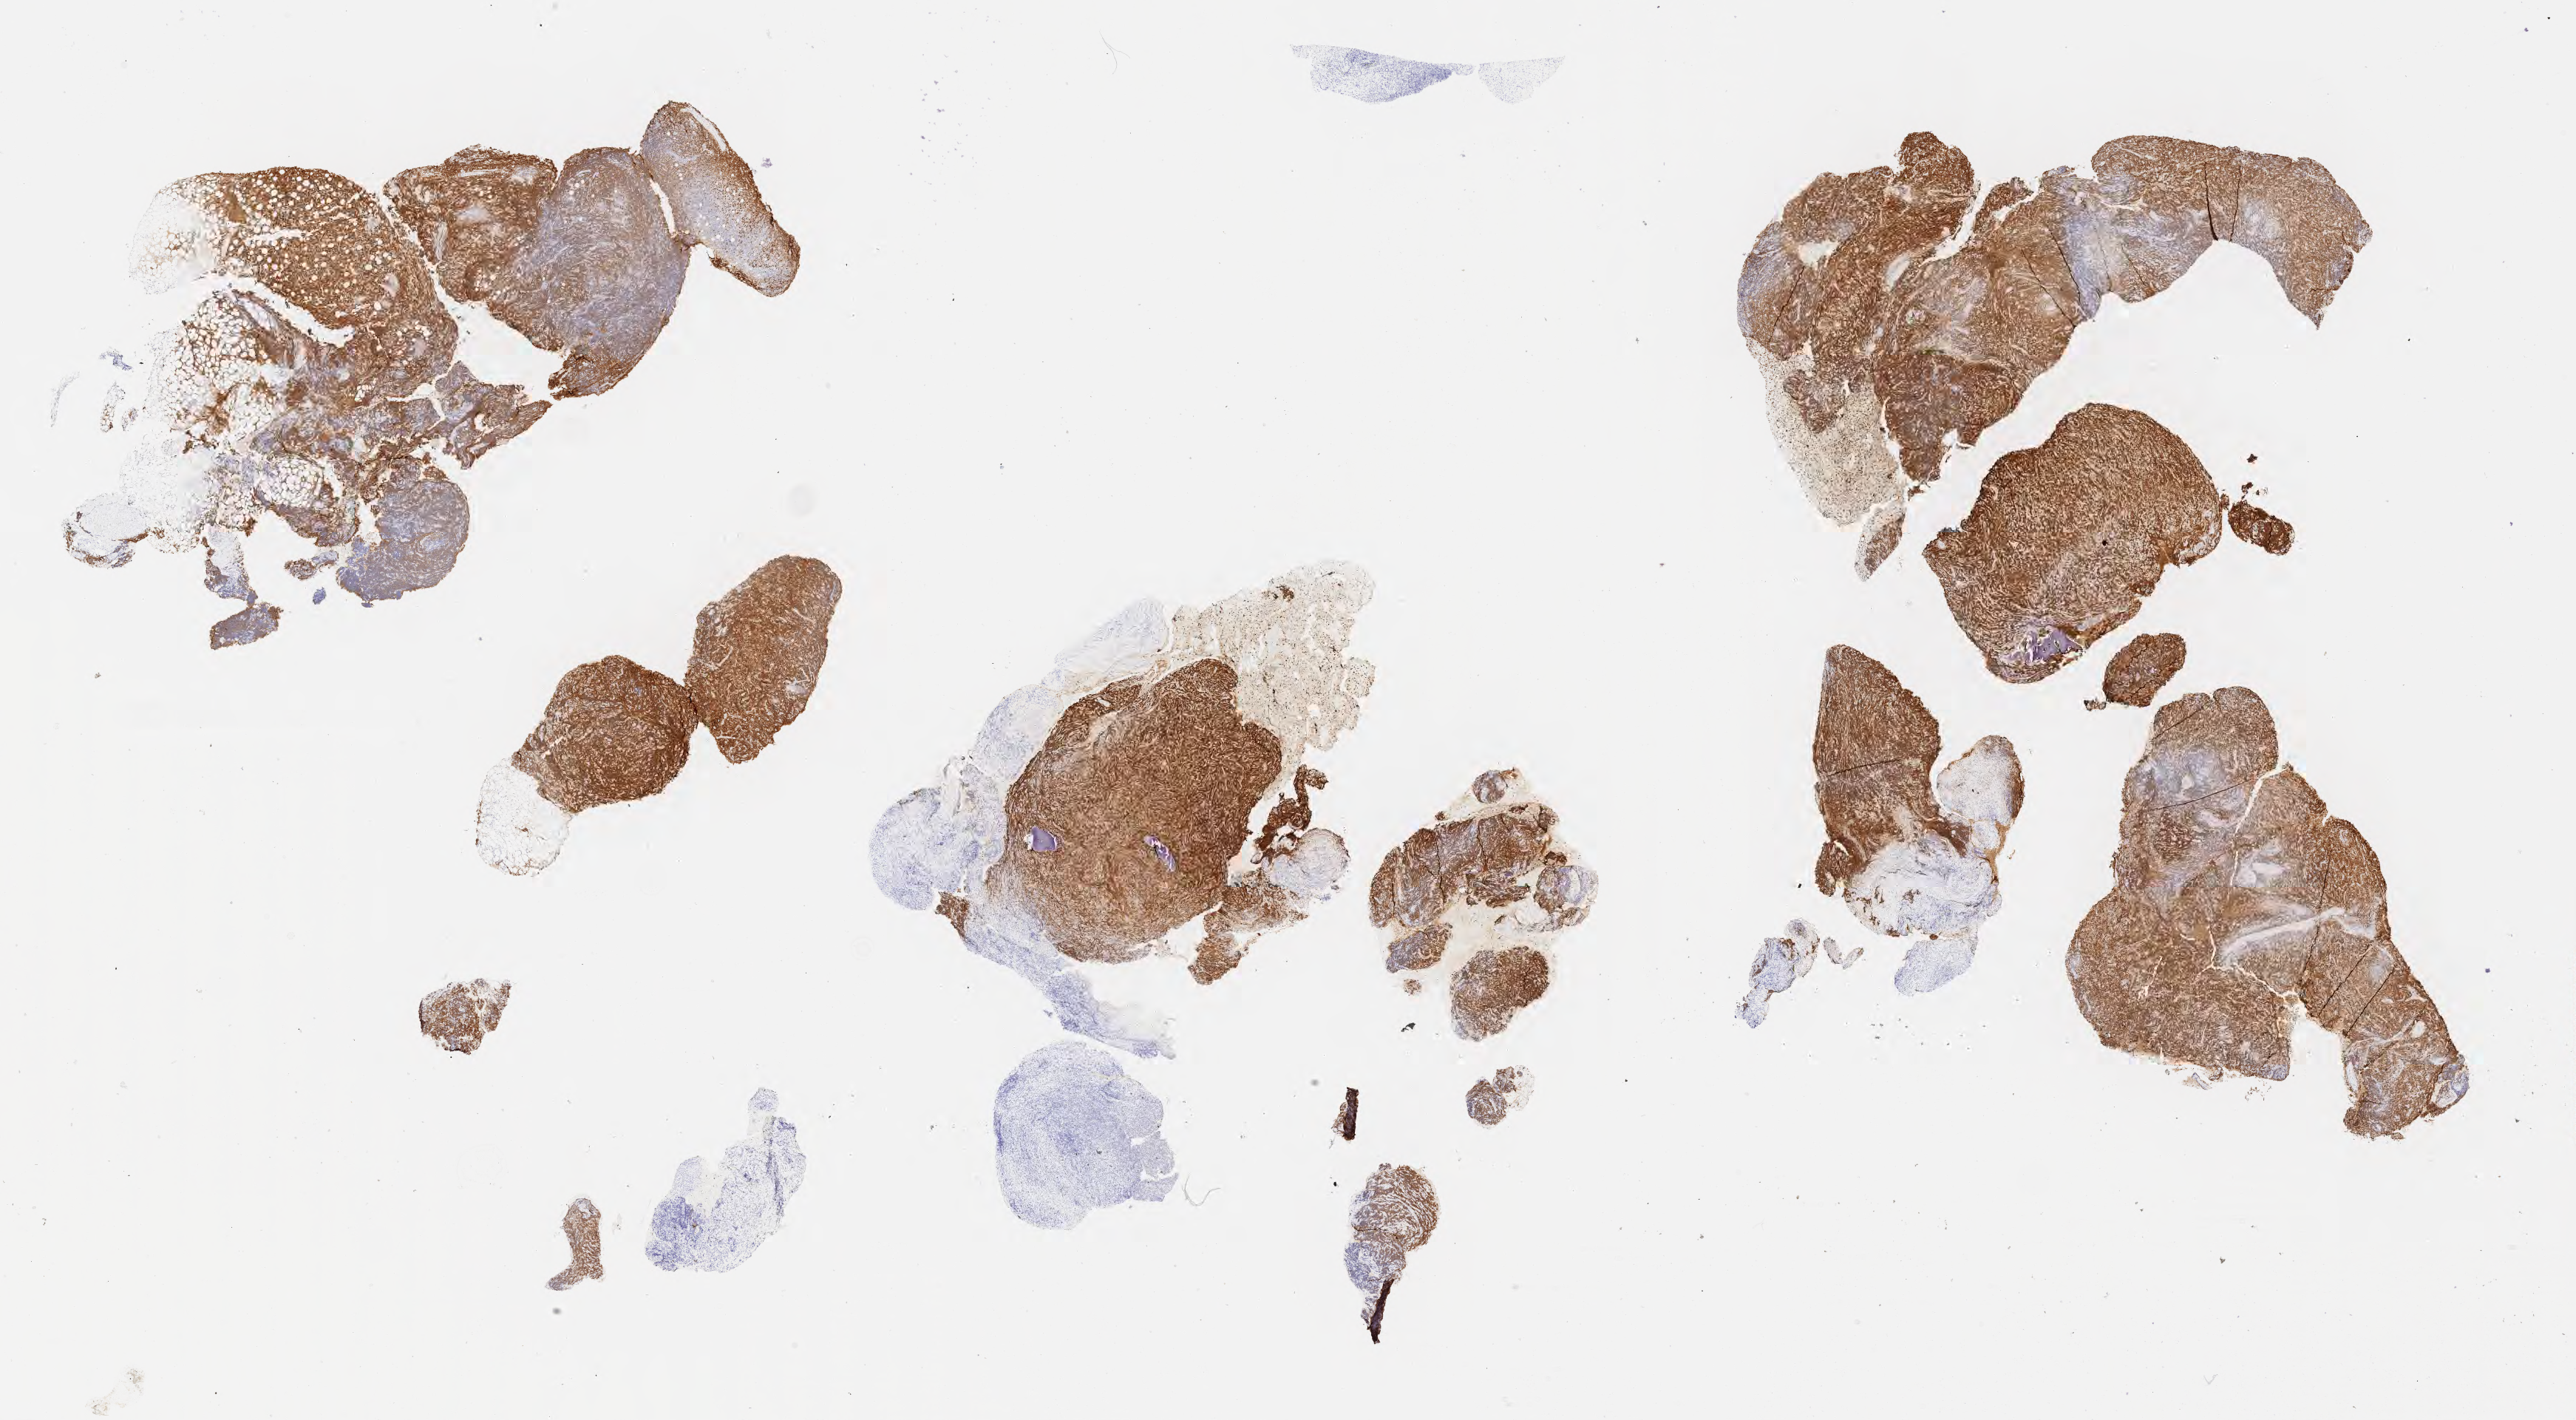
Whole-slide image, immunohistochemical stain for BCL6 — a low-resolution overview of the entire scanned area, about 28.2 x 15.5 mm; tumor tissue. Patient male; aged 45.
Diagnosis: Diffuse large B-cell lymphoma, NOS.